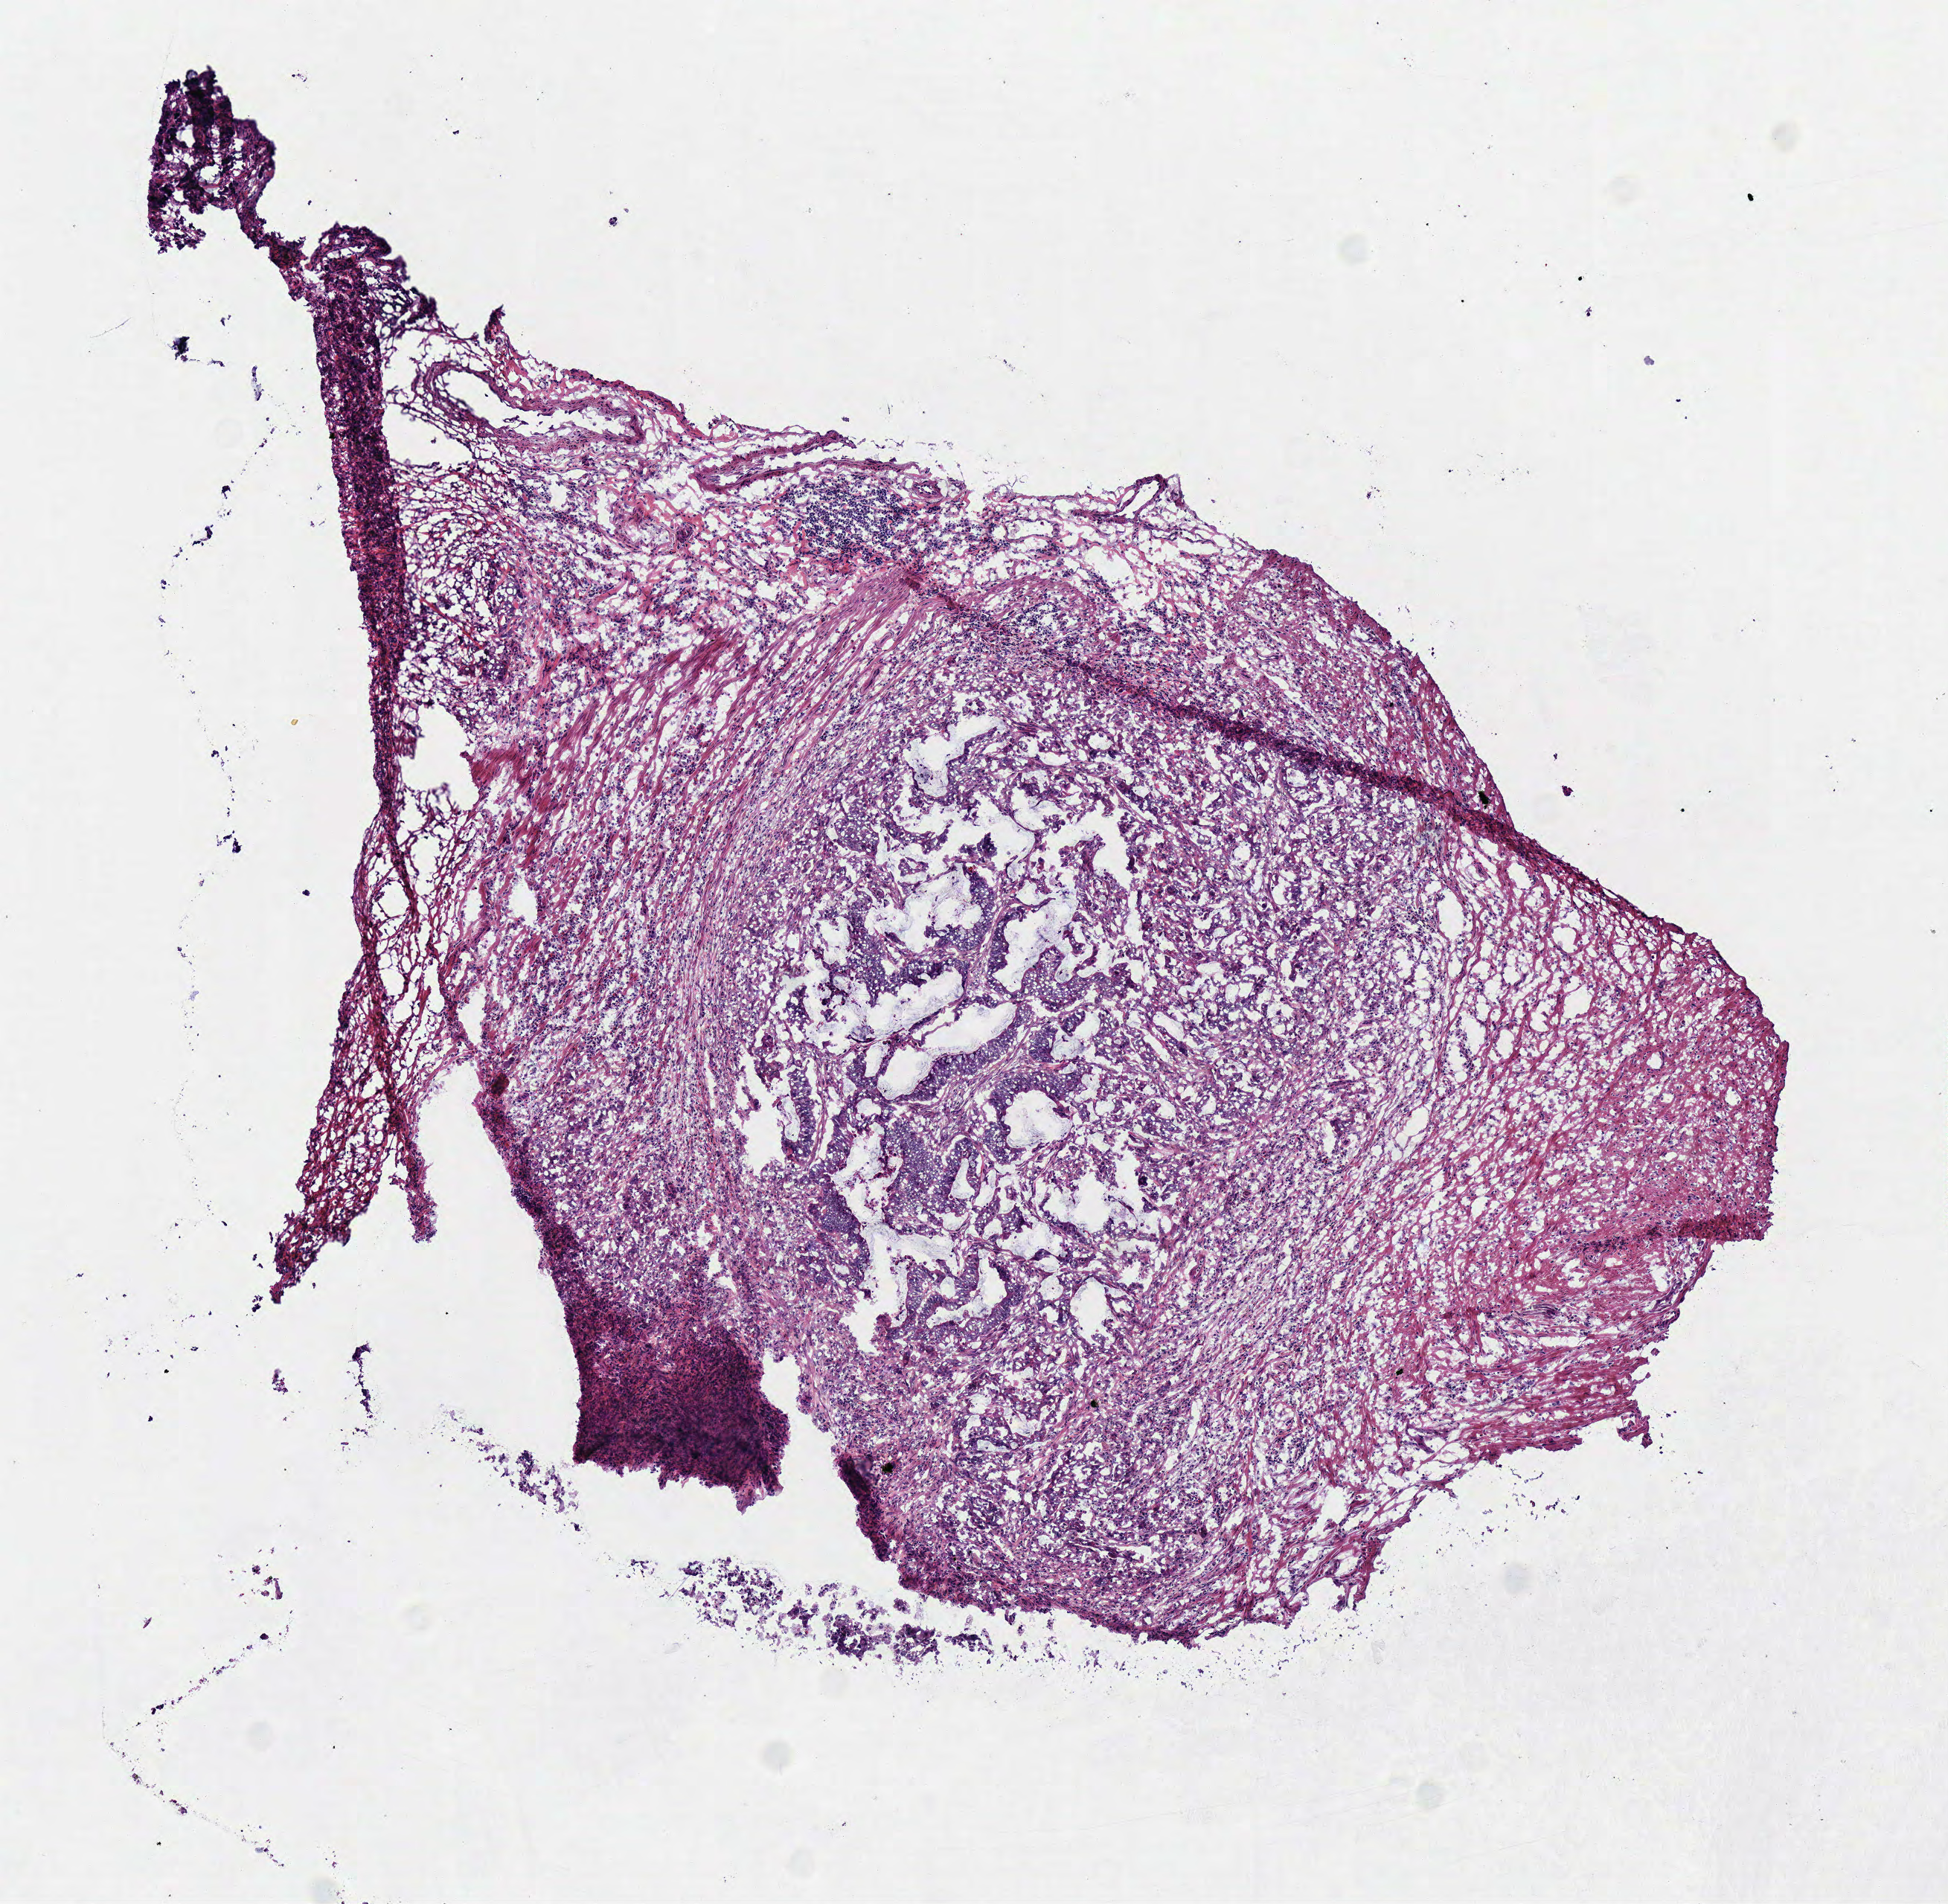
Digitized H&E-stained tissue section (whole slide) — a low-resolution overview of the entire scanned area, about 5.2 x 5.0 mm. Frozen section from the bottom of the tissue portion. Colon, primary tumour sample. Patient: female, age at initial diagnosis 45 years. Slide review estimates, as recorded: tumour cells 70%, tumour nuclei 70%, normal cells 0%, stromal cells 30%, necrosis 0%.
TNM: T3 N1 M0. Lymph nodes positive (case pathology): 3 of 20 examined. AJCC pathologic stage: III. Histologic diagnosis: Adenocarcinoma, NOS (sigmoid colon).